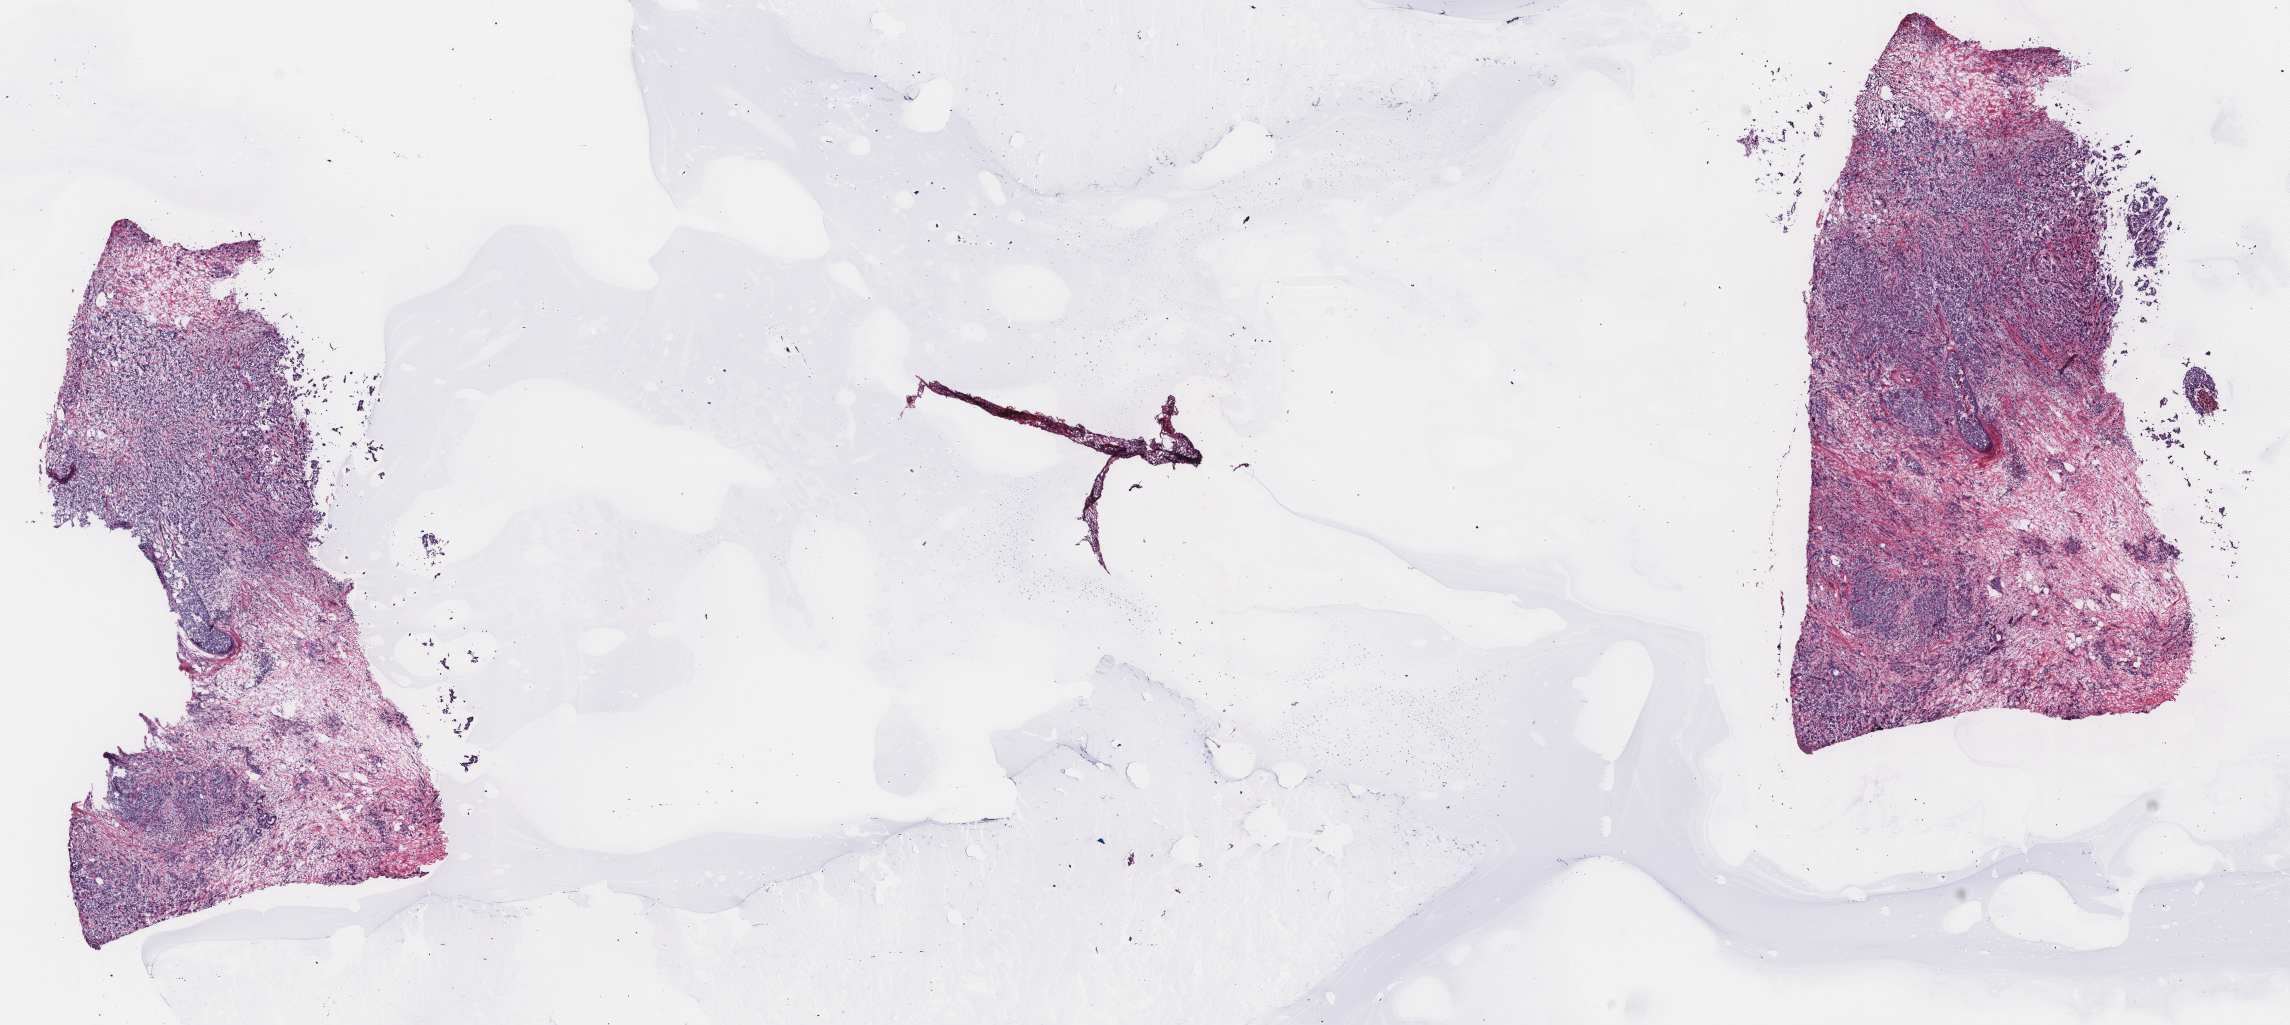
Digitized Hematoxylin and eosin (H&E) stained tissue section (whole slide), low-resolution overview of the scanned area, about 18.2 x 8.1 mm (slide scanned at 40x). Frozen section. Sample: primary tumour, breast. Patient: female, age at initial diagnosis 41 years. Pathologist review of this section (percent, as recorded): tumour cells 70%, tumour nuclei 80%, normal cells 0%, stromal cells 30%, necrosis 0%. Infiltration values recorded for this section: lymphocyte infiltration 0%, monocyte infiltration 0%, neutrophil infiltration 0%.
Pathologic diagnosis: Infiltrating duct carcinoma, NOS. AJCC pathologic stage: IIIC (7th edition). TNM: T2 N3a M0. Lymph nodes positive (case pathology): 11 of 11 examined.